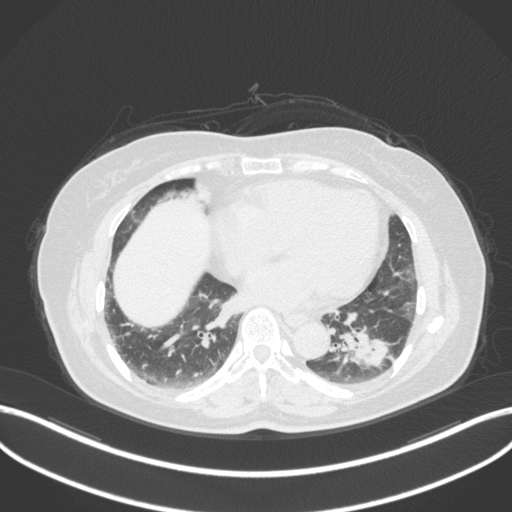
Chest CT, one axial slice; position 142 of 307 along the scan axis; reconstruction kernel B31f; lung window (W 1500 / L -600 HU); 1 mm slice thickness; 512 × 512 image matrix, field of view 400 × 400 mm. Female patient, age 59 years. Case-level facts recorded for this patient, not image findings: clinical TNM (as recorded): T2a N0 M0; histopathological grade: G2-3.
Annotated regions visible in this slice (rectangle marked by the reading radiologist):
- lung tumour (recorded histology: adenocarcinoma): bounding box [x1, y1, x2, y2] px = [338, 318, 394, 376]